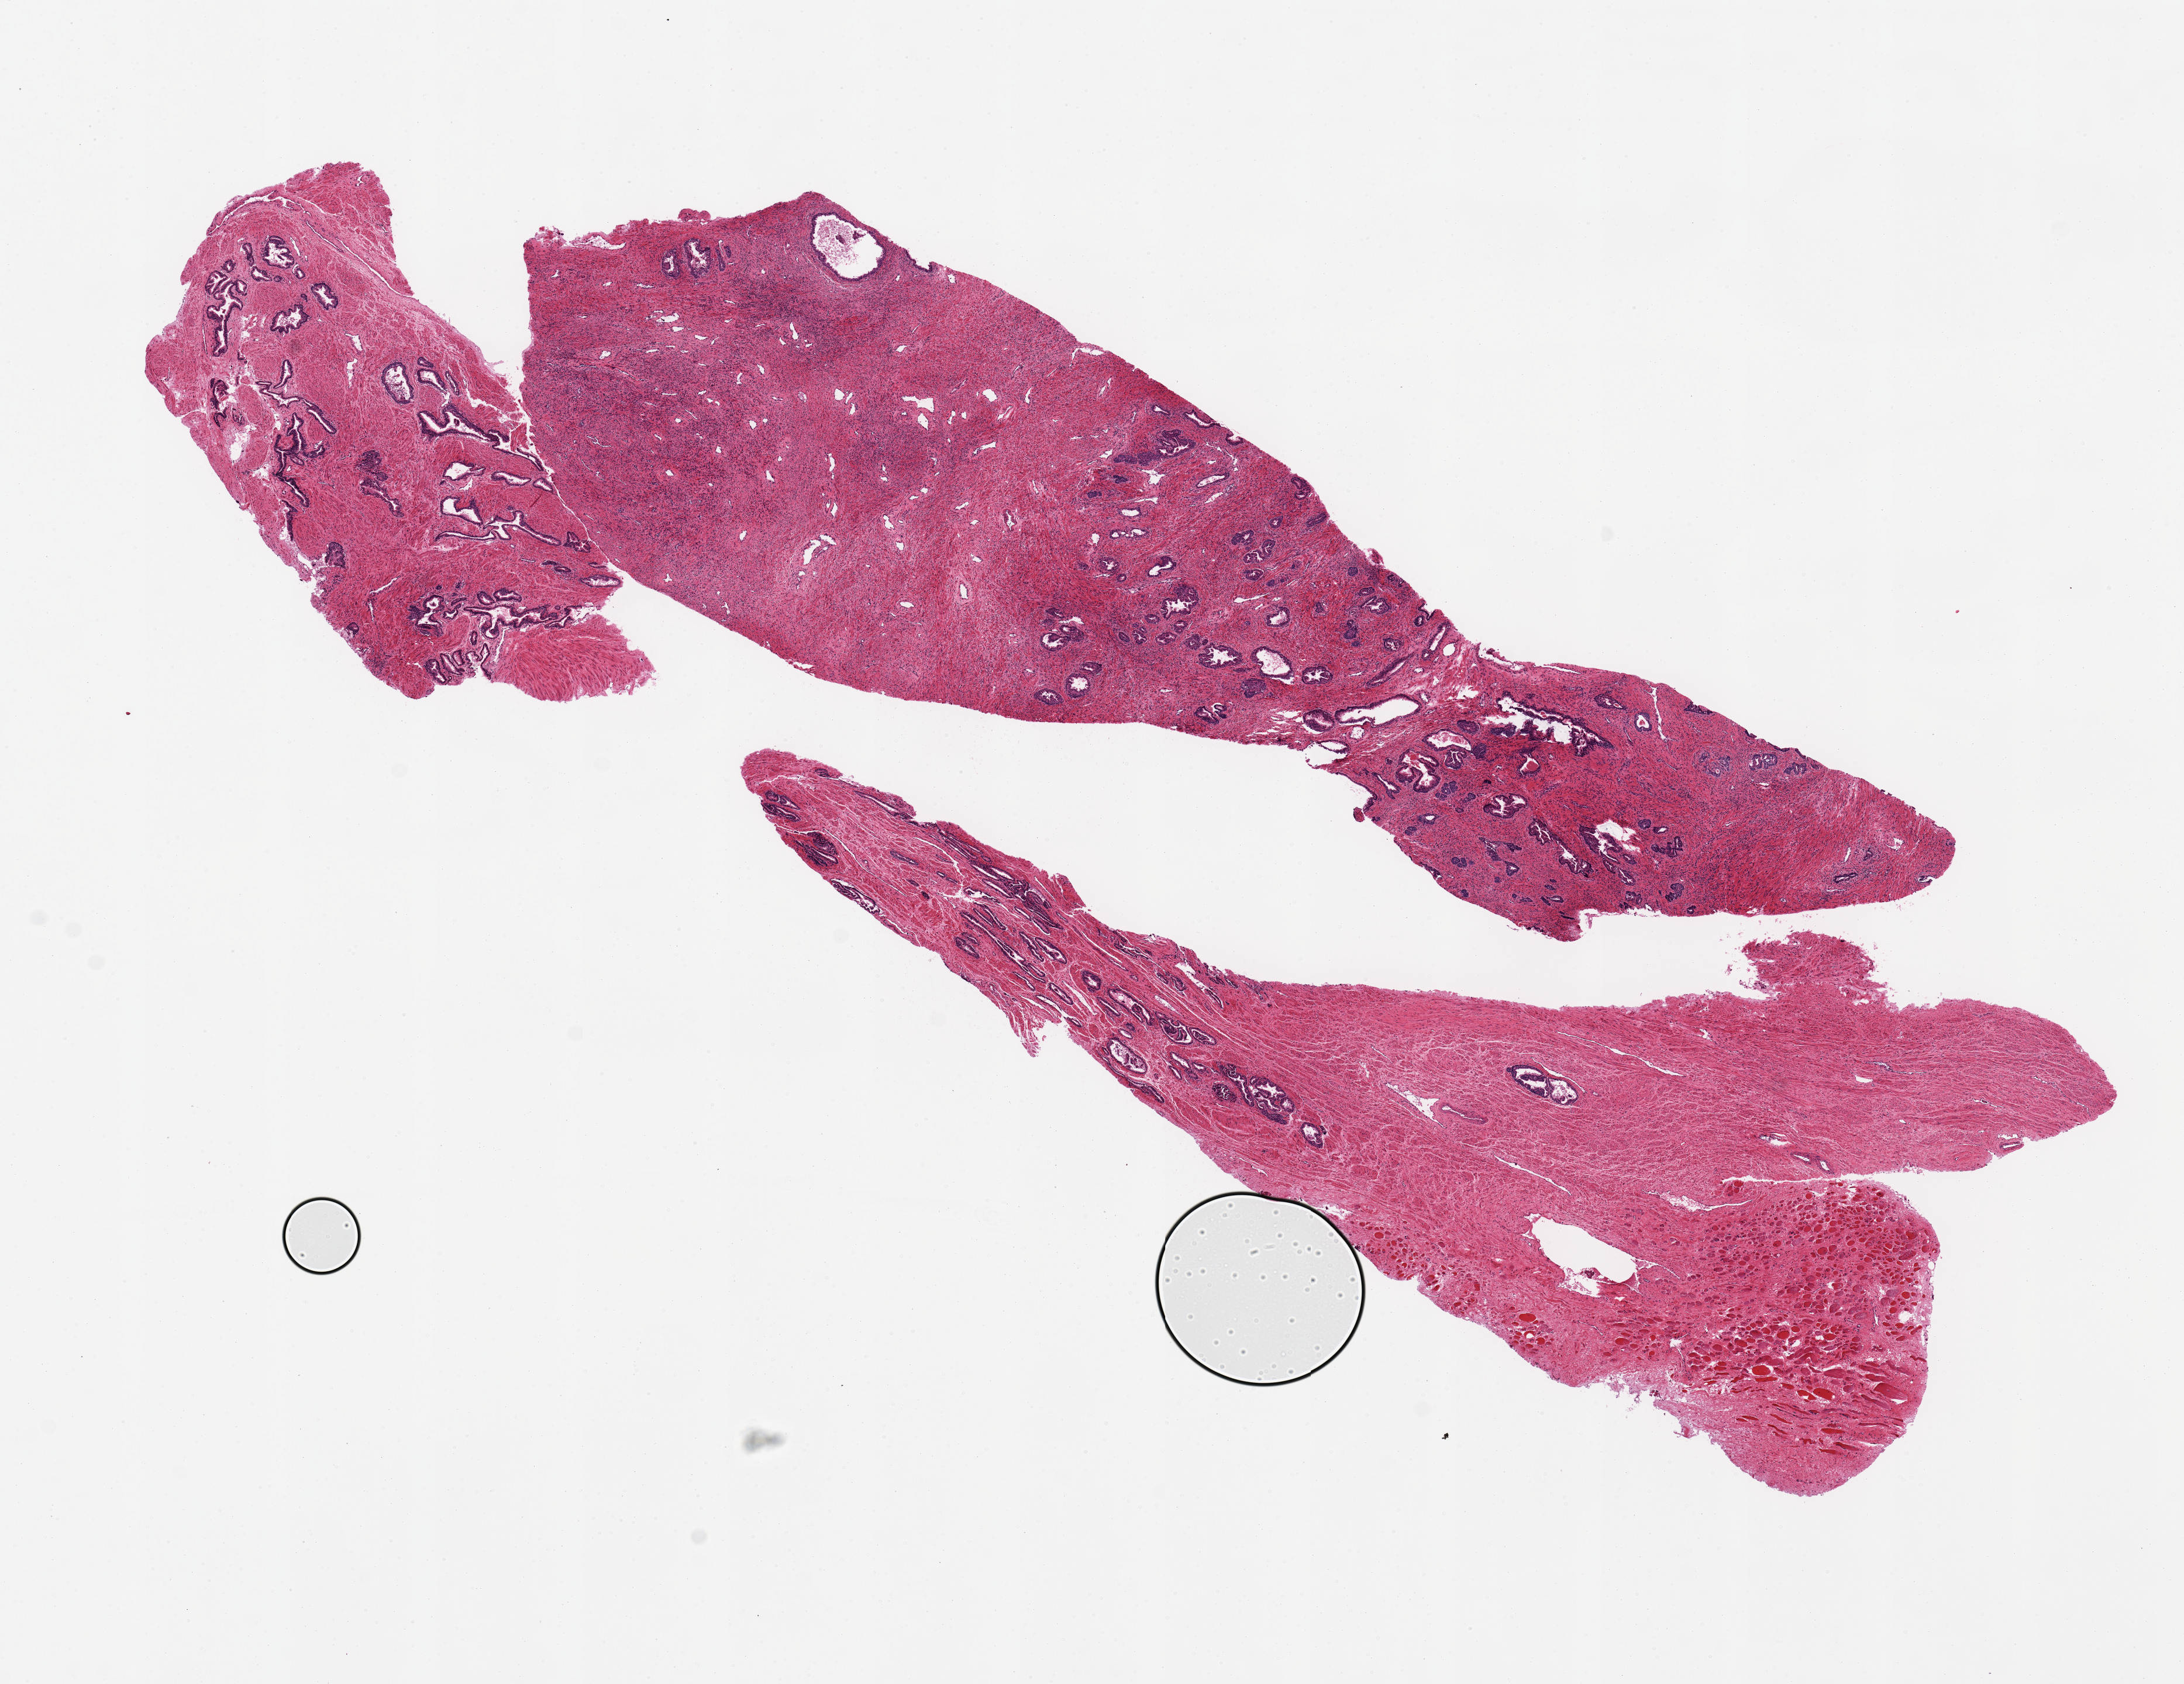
Haematoxylin and eosin whole-slide image, brightfield, shown as a low-resolution overview of the whole scanned area (about 14.8 x 11.4 mm), PAXgene-fixed paraffin-embedded (PFPE) section, target tissue: prostate, tissue donor sample. Male donor.
Pathologist's review note for this sample: Peripheral specimen, glandular atrophy.